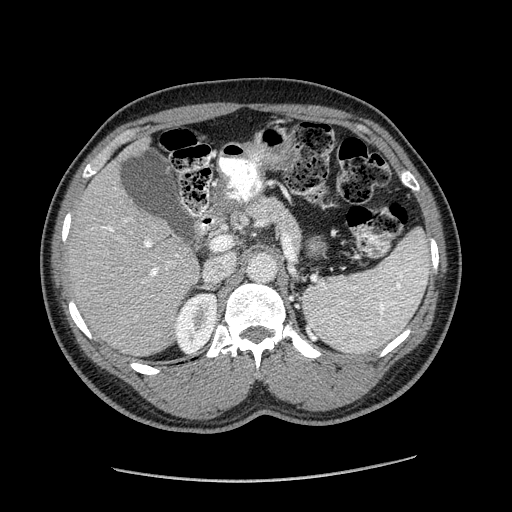
Contrast-enhanced abdominal CT (liver protocol), one axial slice. Slice 105 of 182 in the series (ordered by position). Reconstruction kernel STANDARD. Soft-tissue window (W 400 / L 40 HU). 512 × 512 image matrix, field of view 400 × 400 mm. Case-level facts recorded for this patient, not image findings: diagnosis: hepatocellular carcinoma (patient treated with transarterial chemoembolisation; whether this scan precedes or follows treatment is not stated here); TNM stage (as recorded): Stage-I; Child-Pugh class: A.
Outlined on this slice (semi-automatic segmentation, software-assisted and operator-edited):
- liver parenchyma outside the tumour (the mass and vessels are separate outlines, so this box may not span the whole liver): bounding box <66,138,199,356> (left, top, right, bottom; pixels)
- mass: <97,232,131,267>
- liver vessels: <102,221,179,277>